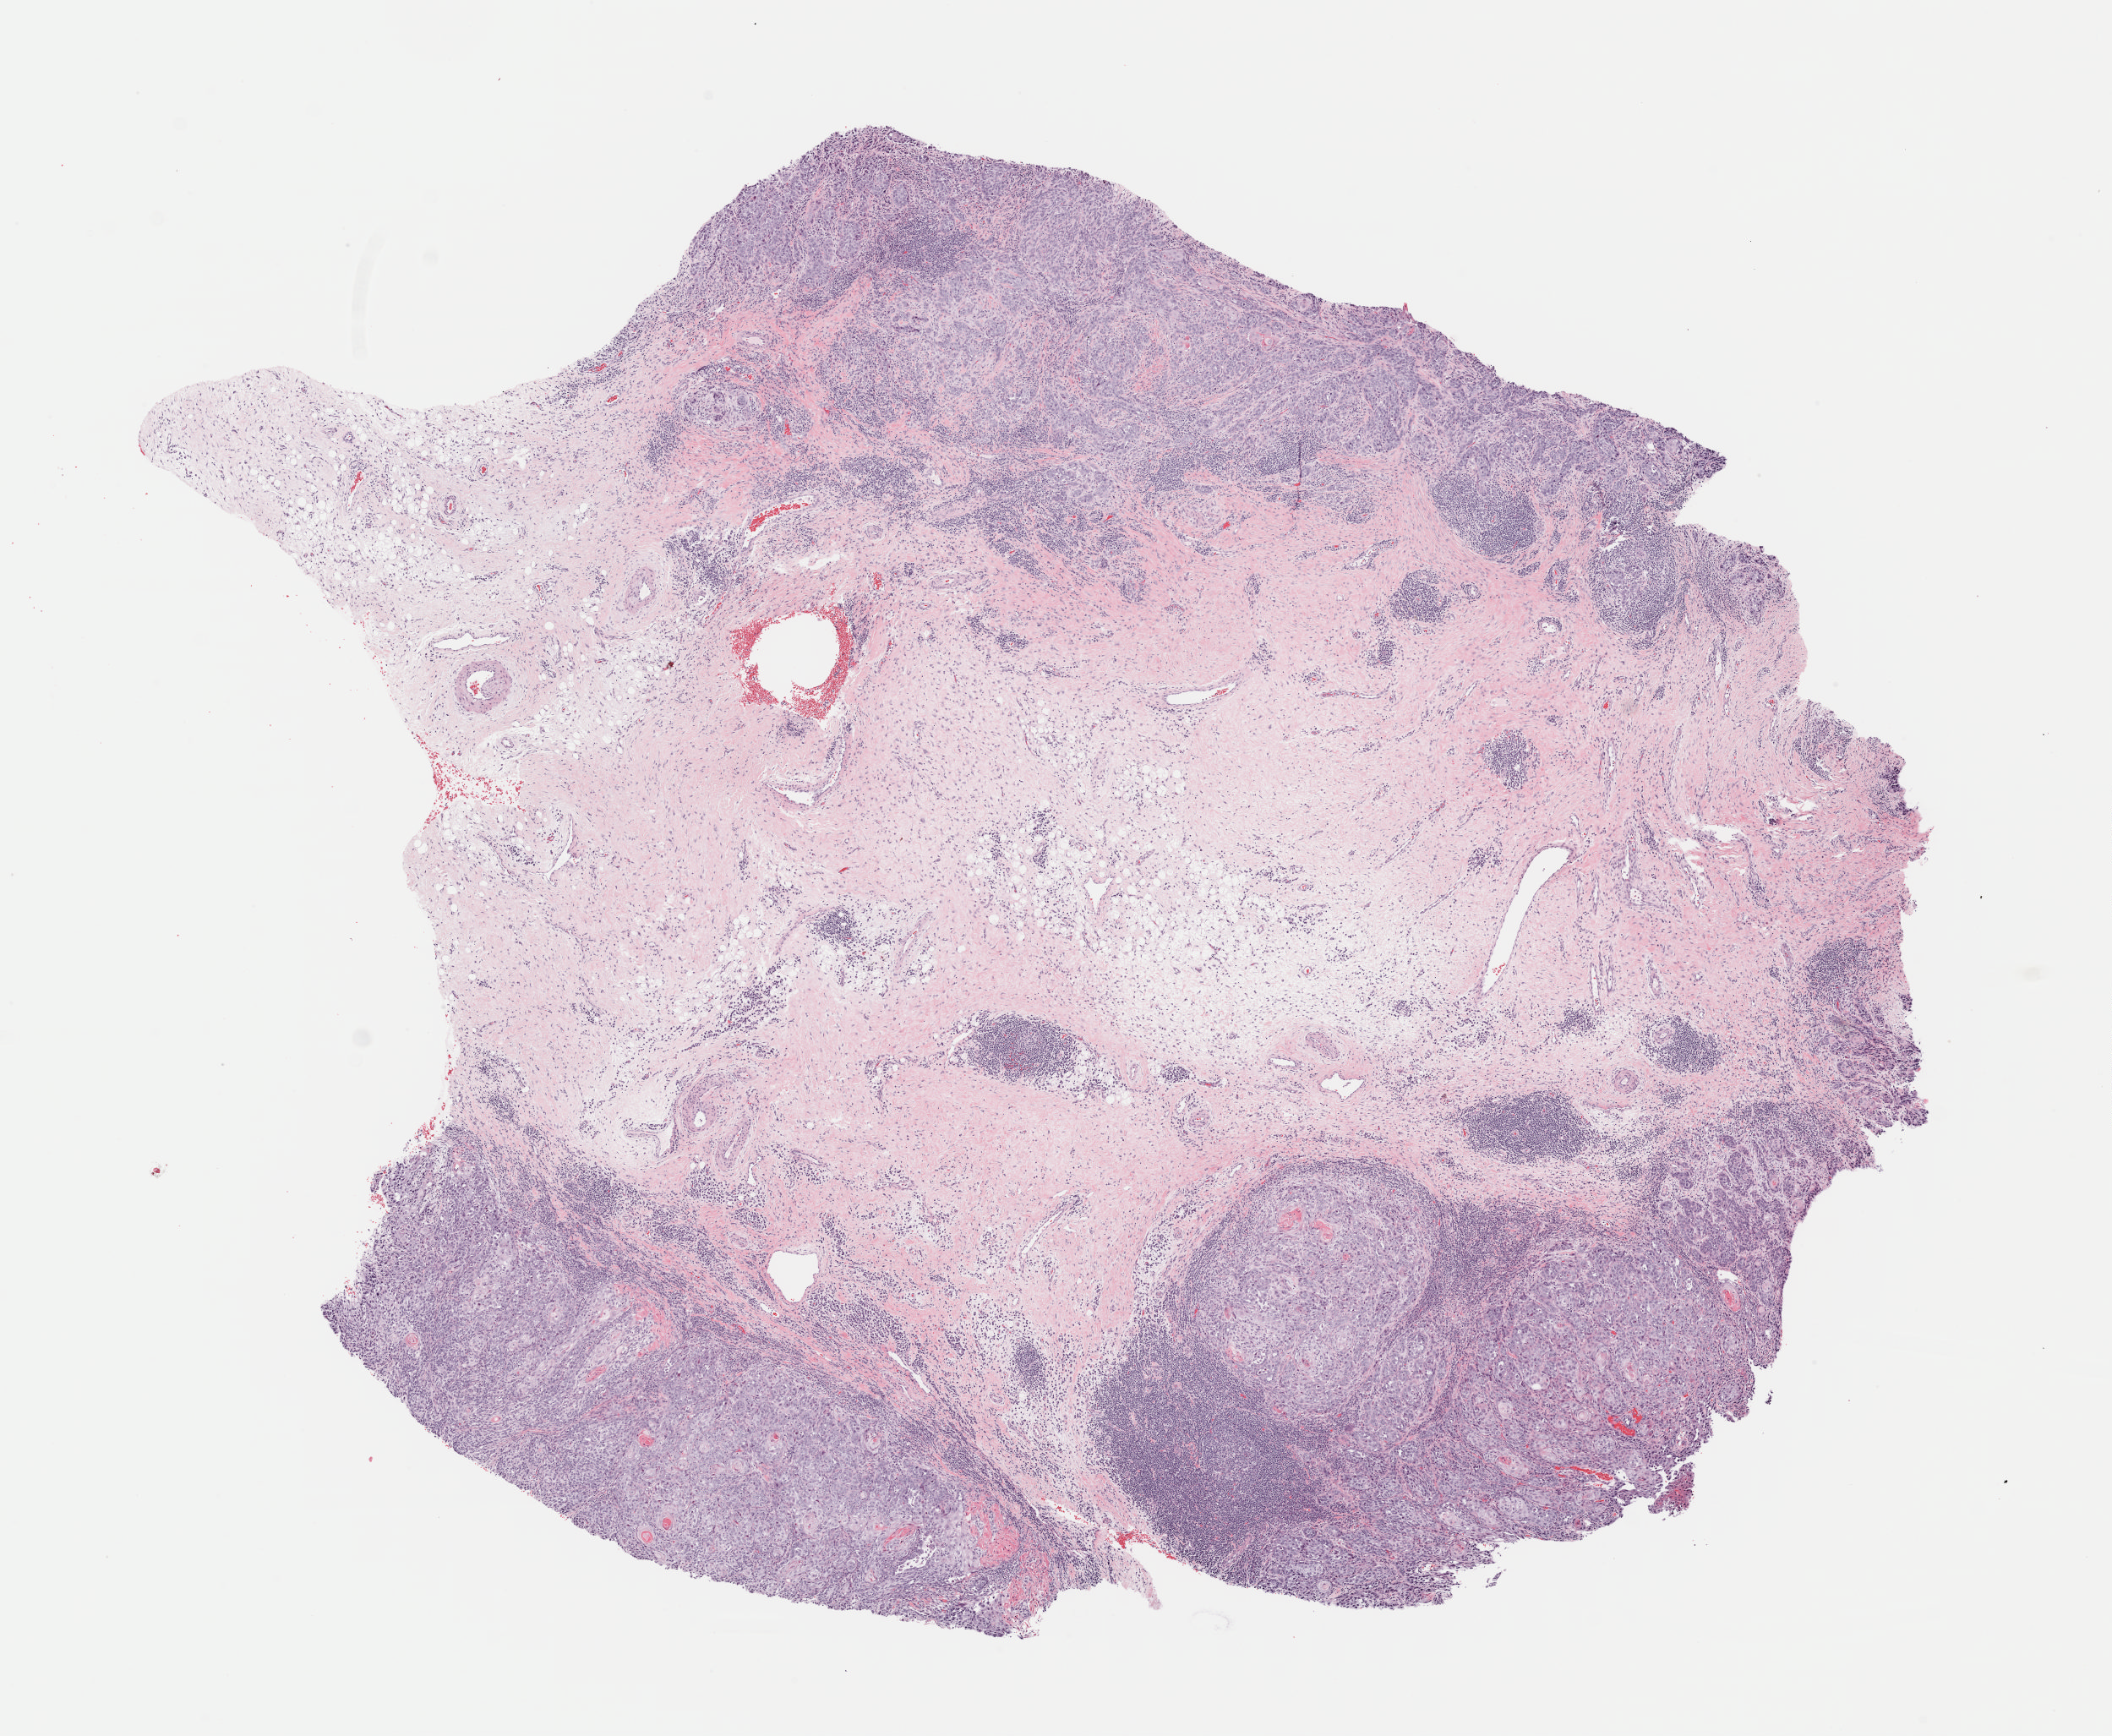
Whole-slide histology image, Hematoxylin and eosin (H&E) stained — shown as a low-resolution overview of the whole scanned area (about 9.9 x 8.1 mm, from a 40x scan). Formalin-fixed paraffin-embedded (FFPE) diagnostic section. Head and neck, primary tumour sample. Patient: male, age at initial diagnosis 60 years. Histologic grade: G3 (poorly differentiated).
Histologic diagnosis: Squamous cell carcinoma, NOS (larynx, NOS). AJCC pathologic stage: IVA (7th edition). TNM: T3 N2b MX.